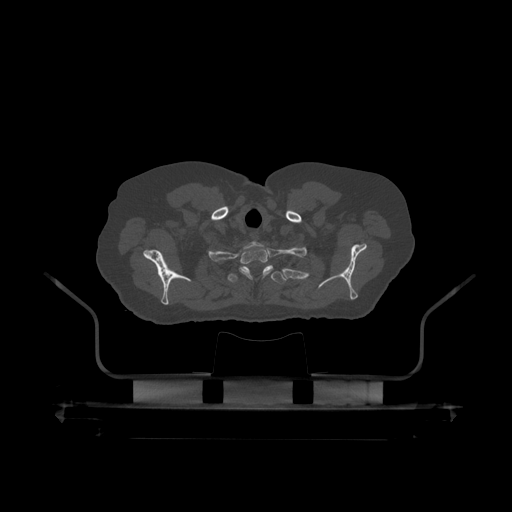
CT including the spine, one axial slice; slice 386 of 390 in the series (ordered by position); reconstruction kernel STANDARD; 120 kVp; bone window (W 1800 / L 400 HU); 1.25 mm slice thickness; 512 × 512 image matrix, field of view 650 × 650 mm. Male patient, age 60 years. Case-level facts recorded for this patient, not image findings: primary cancer: prostate.
Outlined on this slice (semi-automatically segmented with operator editing):
- T1 vertebra: bounding box (x1, y1, x2, y2) in pixels: (240, 242, 272, 280)
- T2 vertebra: (228, 266, 287, 284)